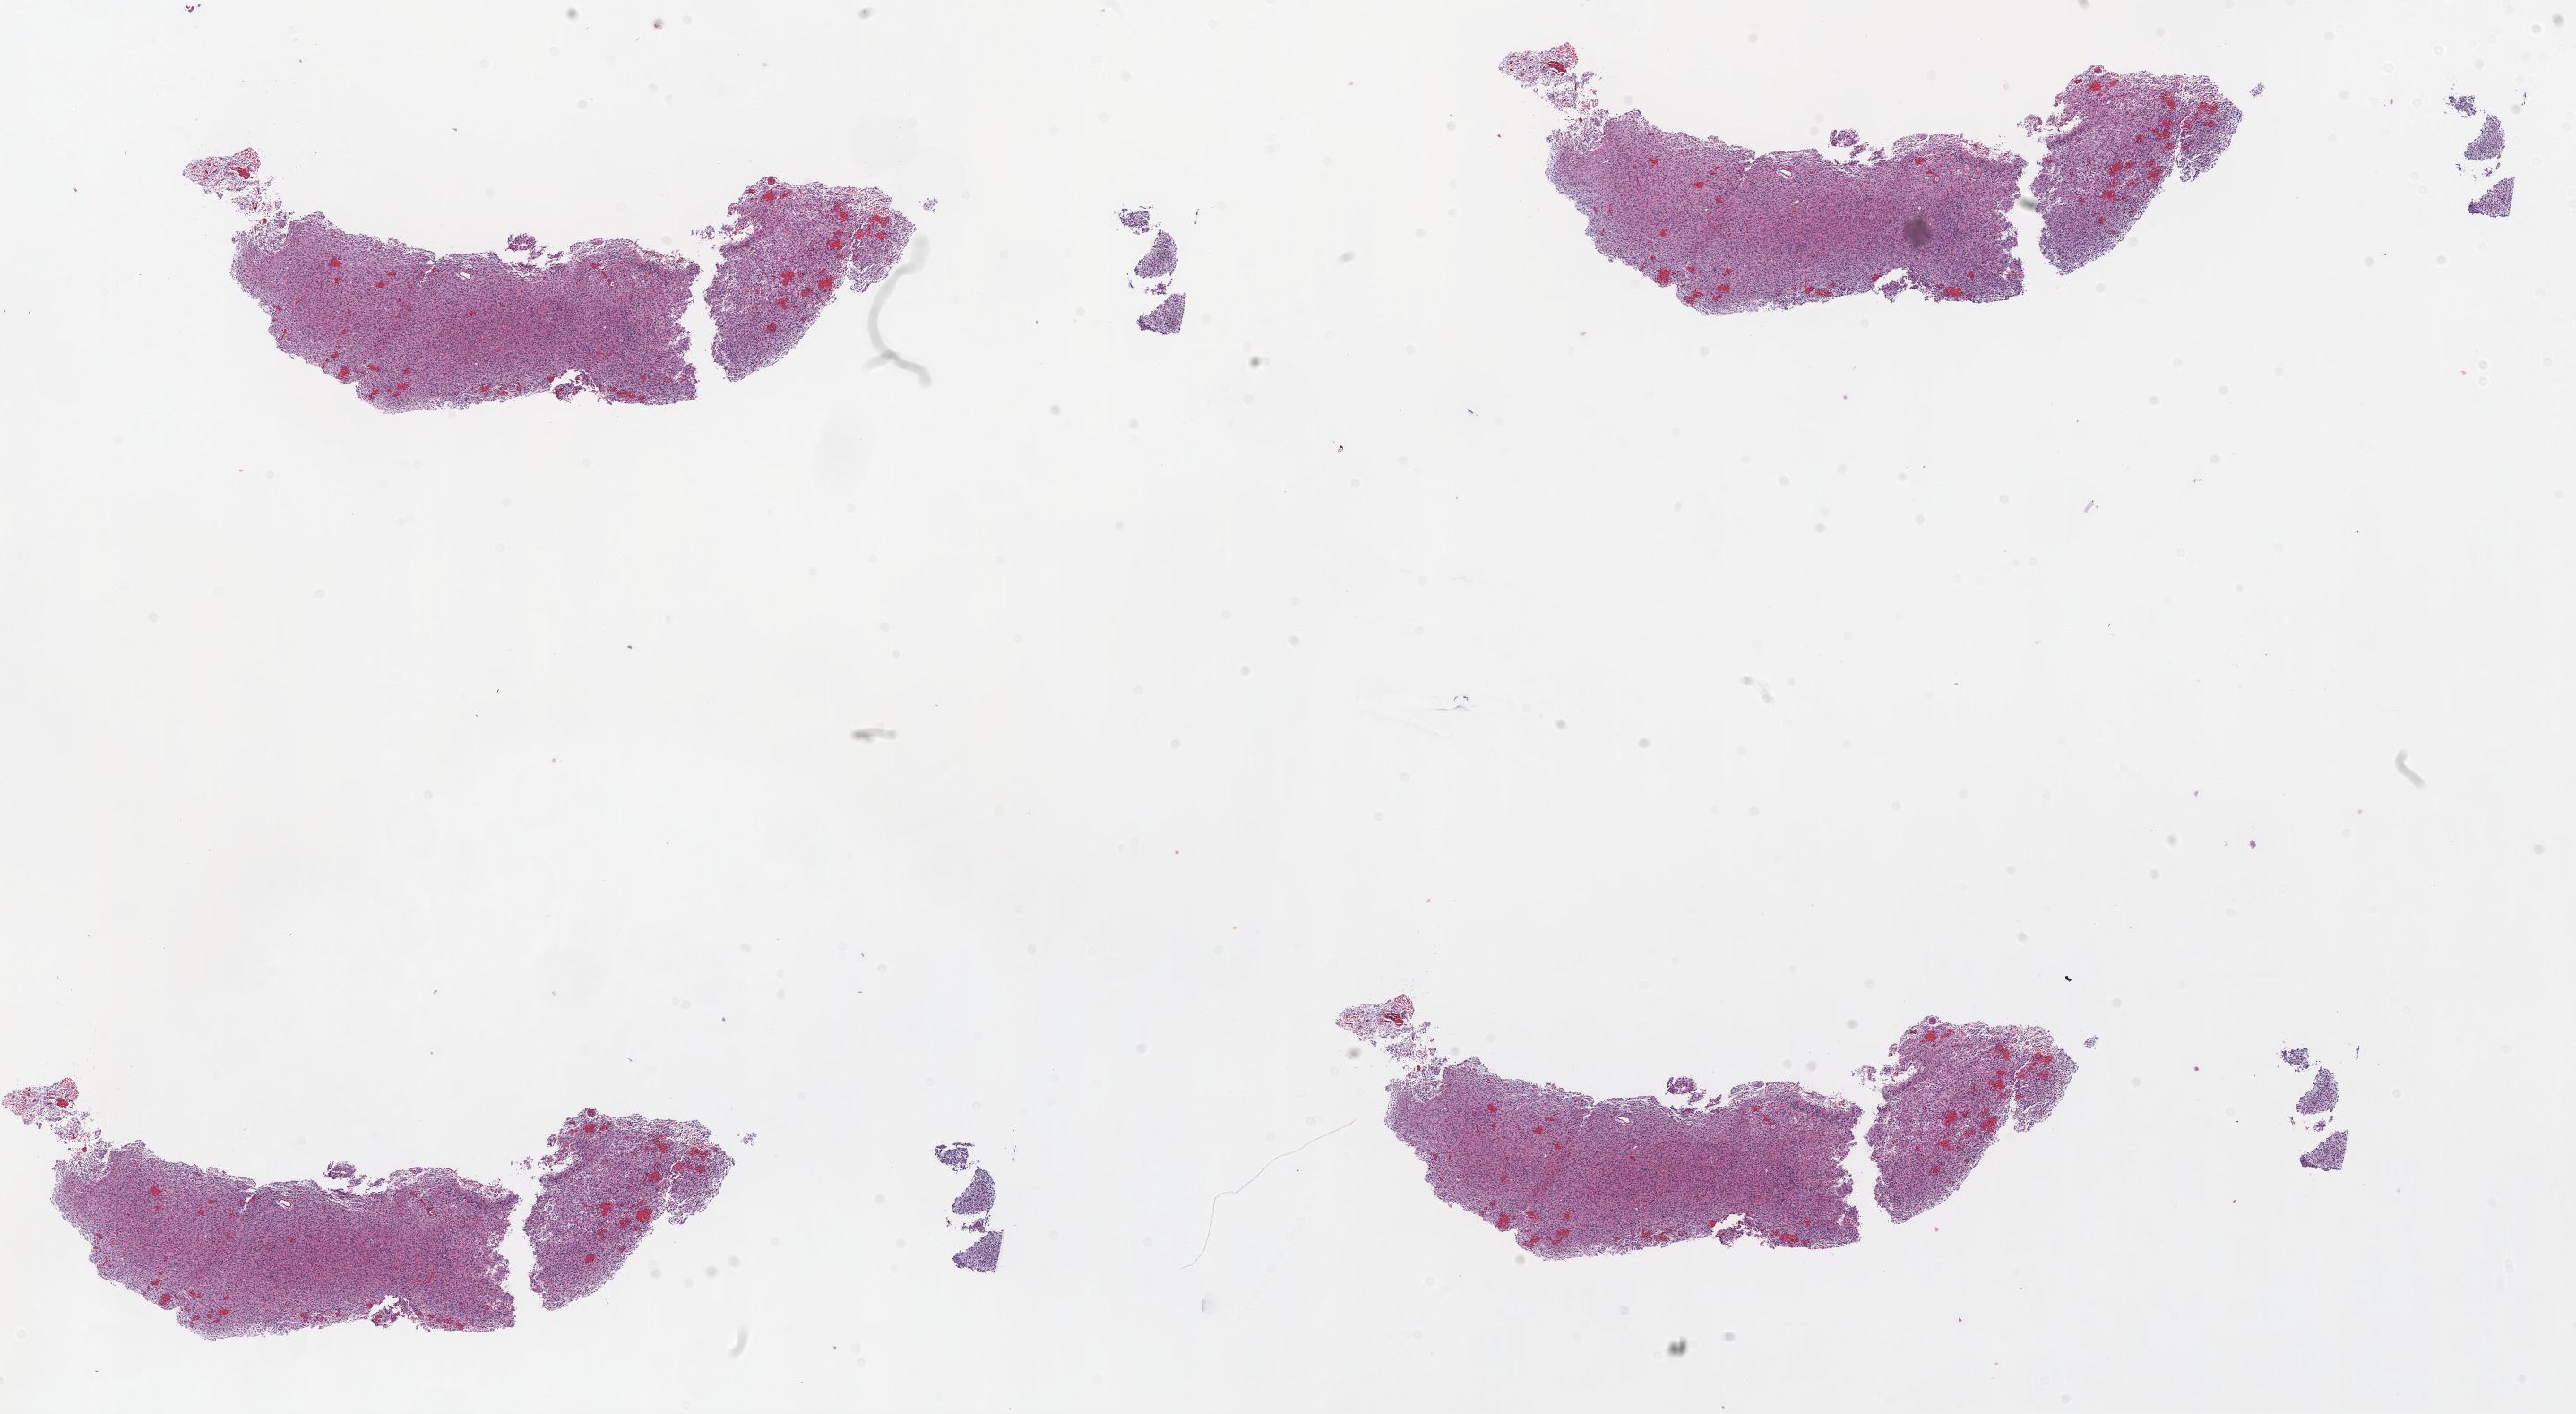
Digitized H&E-stained tissue section (whole slide) — low-resolution overview of the scanned area, about 23.1 x 12.7 mm (from a 20x scan); FFPE section; sample: primary tumour, brain. Male patient; age at initial diagnosis 52 years.
Histologic diagnosis: Glioblastoma.